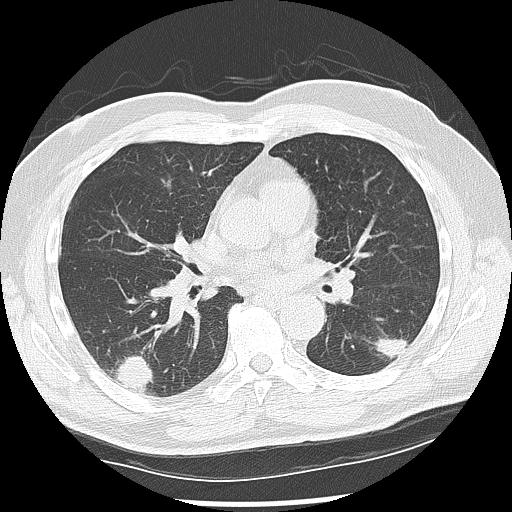
Low-dose screening chest CT, one axial slice. Slice 68 of 142 in the series (ordered by position). Reconstruction kernel LUNG. 120 kVp. Lung window (W 1500 / L -600 HU). 512 × 512 image matrix, field of view 360 × 360 mm.
Structures marked on this image (manually delineated by an expert):
- lesion 1 (nodule, lower lobe of left lung): bounding box (x1, y1, x2, y2) in pixels: (374, 336, 409, 360)
- lesion 2 (nodule, lower lobe of right lung): (113, 355, 154, 394)